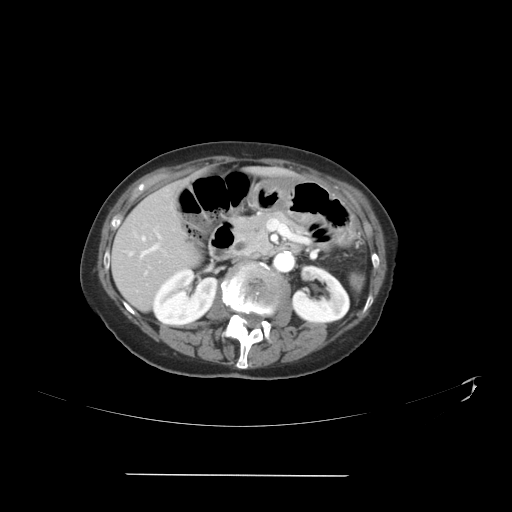
Contrast-enhanced abdominal CT, one axial slice. 120 kVp. Intravenous contrast given. Soft-tissue window (W 400 / L 40 HU). 512 × 512 image matrix, field of view 431 × 431 mm. Female patient, age 74 years. Case-level facts recorded for this patient, not image findings: diagnosis: colorectal cancer liver metastases, imaged before liver resection; multiple liver metastases: yes.
Structures marked on this image (outlined manually by an expert reader):
- hepatic veins: bounding box (x1, y1, x2, y2) in pixels: (129, 237, 147, 275)
- liver: (112, 186, 195, 308)
- planned liver remnant (the part of the liver to remain after resection): (119, 186, 186, 247)
- portal vein (with intrahepatic branches): (141, 234, 160, 256)